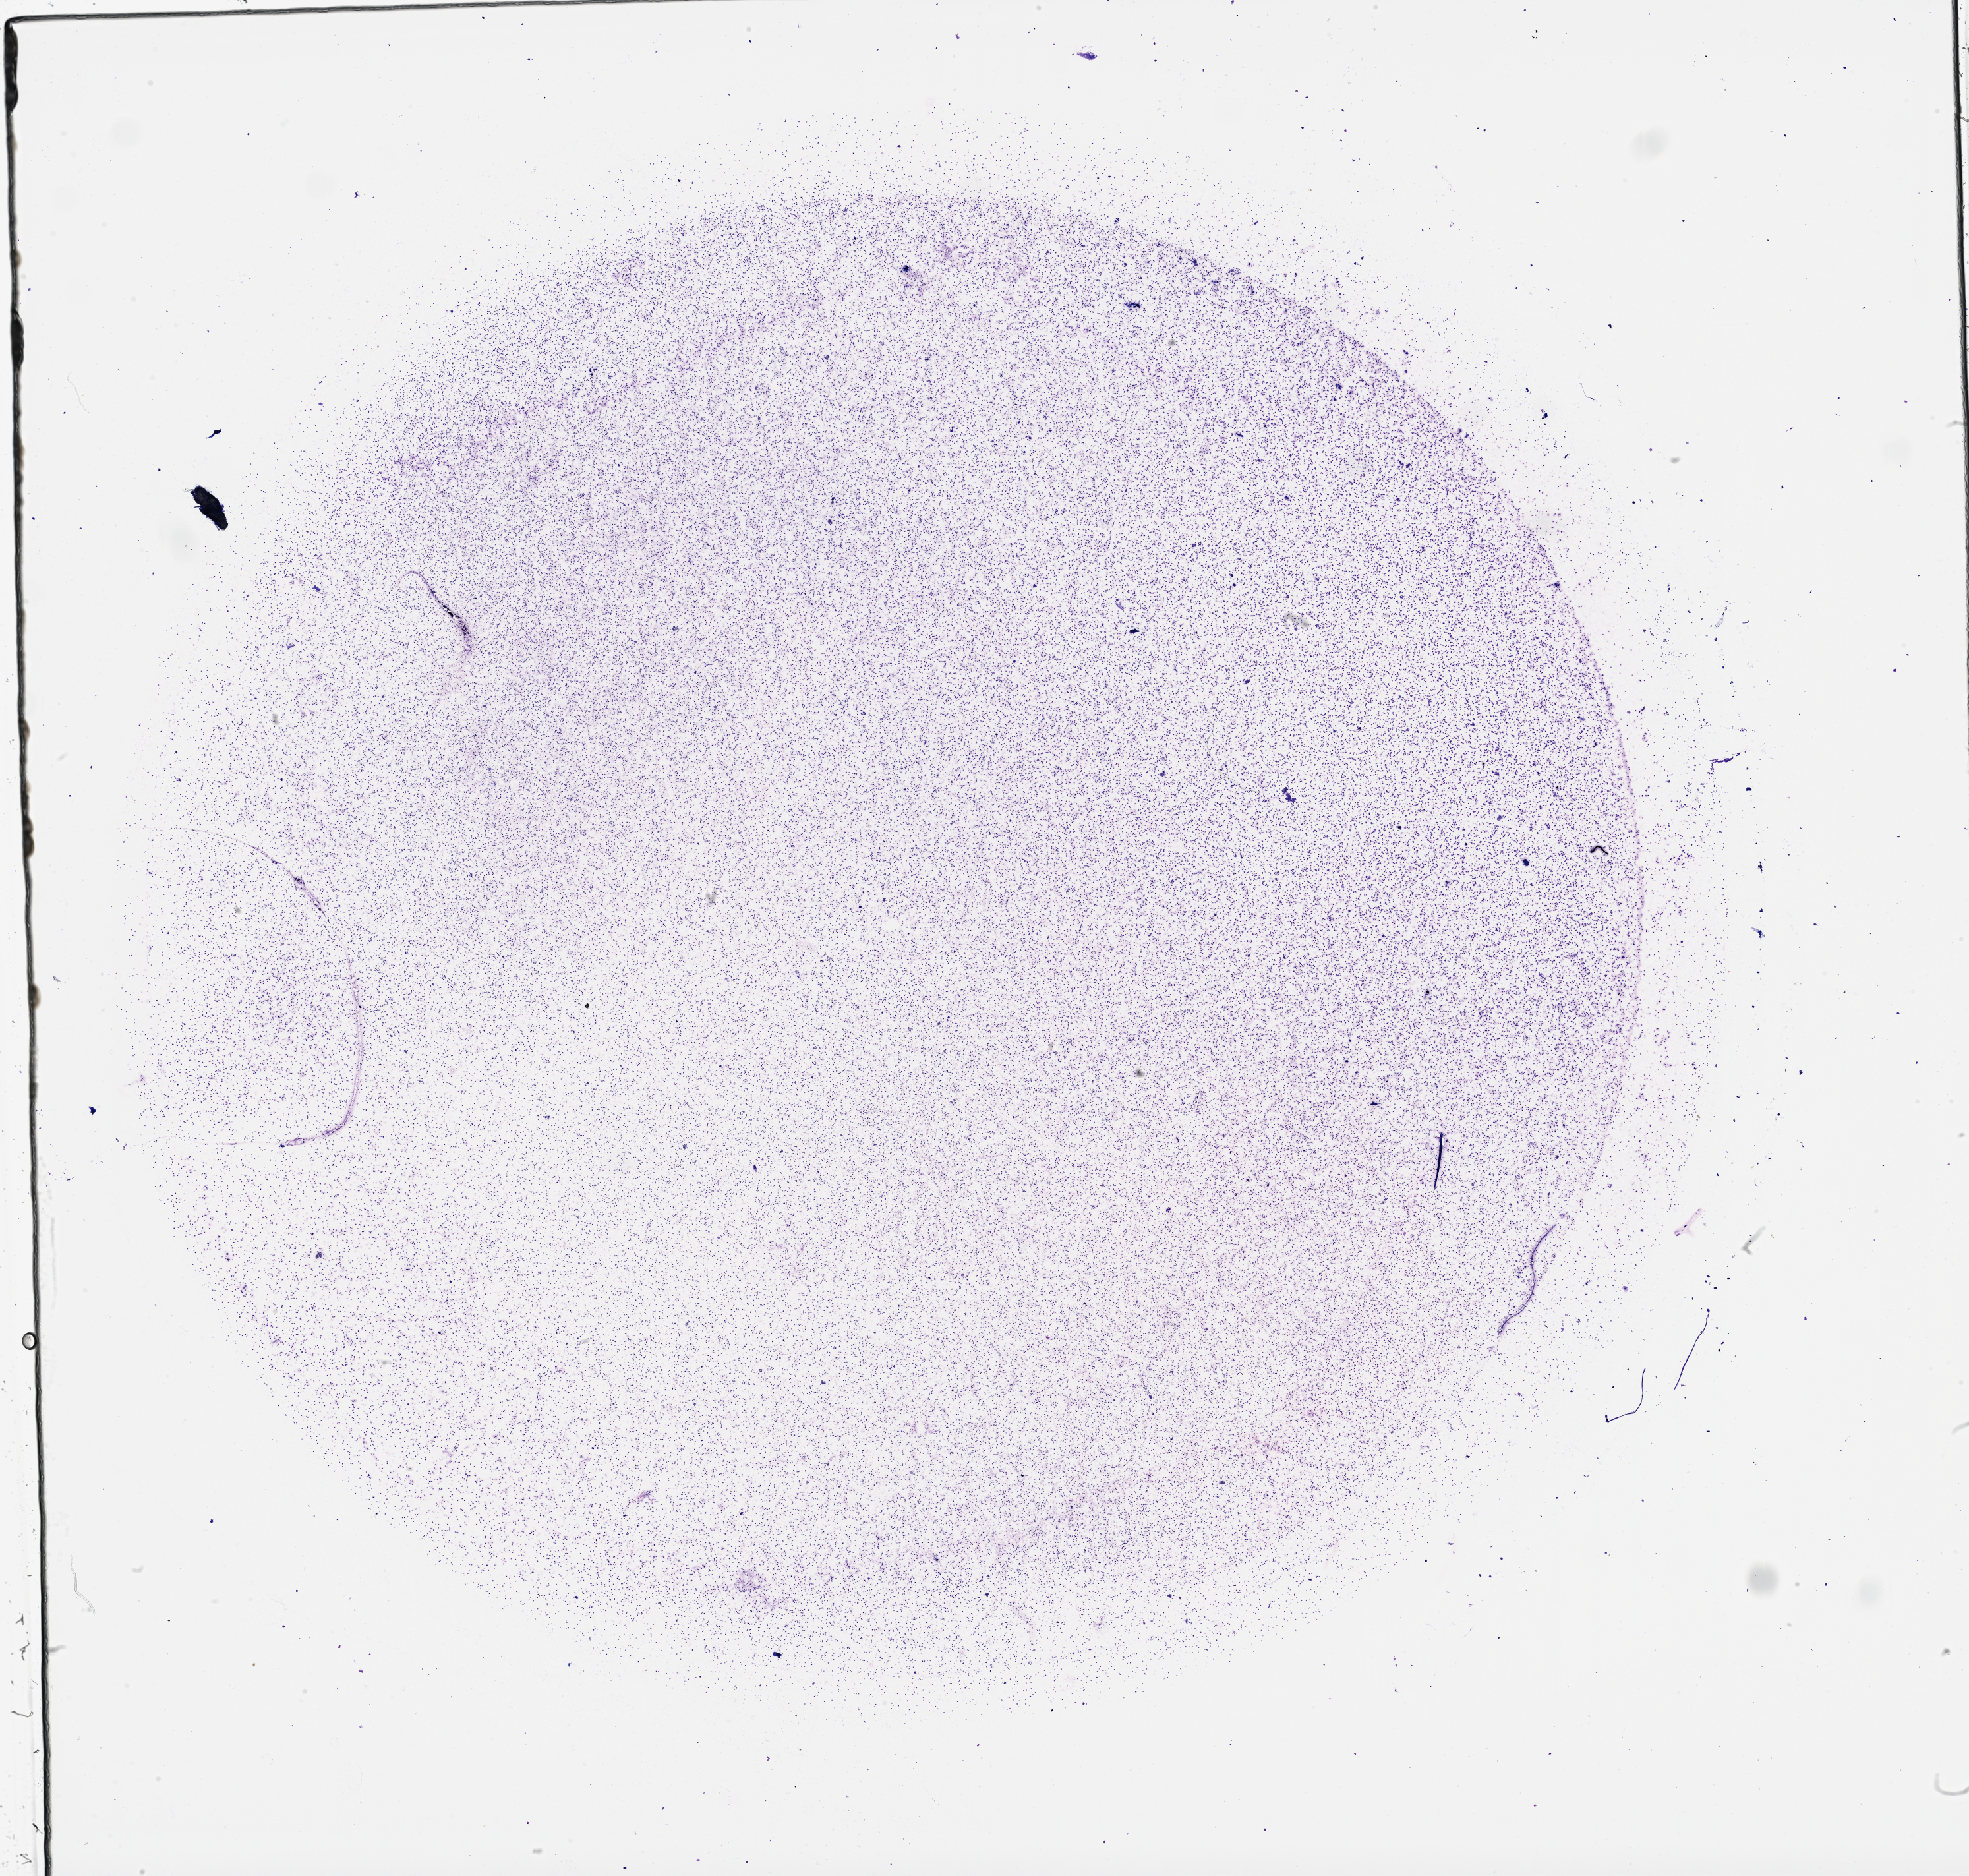
Whole-slide histology image, H&E — whole scanned area (about 24.1 x 23.0 mm, acquisition: 40x scan) shown as a low-resolution overview; bone marrow (leukaemic) sample. 58-year-old female patient. Blasts: 20%.
* diagnosis: Acute Myeloid Leukemia
* WHO classification: AML with minimal differentiation
* FAB classification: M0